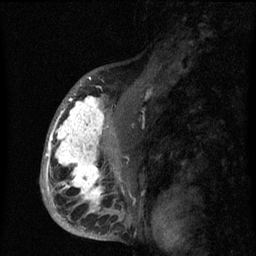
Breast MRI (dynamic contrast-enhanced), one sagittal slice; dynamic contrast-enhanced series, image 2 of 3 at this slice position (ordered by acquisition); 1.5 T; TE 4.2 ms, TR 8 ms; 2 mm slice thickness; 256 × 256 image matrix. Patient: female, 50 years.
Structures marked on this image (semi-automatically segmented with operator editing):
- analysis volume of interest (the breast-tissue region the enhancement analysis was run in; not a lesion): box from (x=43, y=90) to (x=142, y=216) px
- tumour enhancement mask (voxels above the 70 % enhancement threshold inside the analysis volume of interest): (x=44, y=93)–(x=105, y=213)